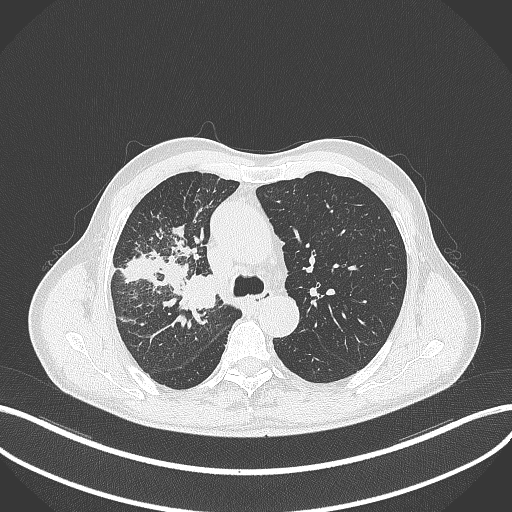
Chest CT, one axial slice. Slice 331 of 490 in the series (ordered by position). 120 kVp. Lung window (W 1500 / L -600 HU). 512 × 512 image matrix, field of view 400 × 400 mm. Patient: male, 69 years. Case-level facts recorded for this patient, not image findings: clinical TNM (as recorded): T2a N0 M0.
Outlined on this slice (rectangle marked by the reading radiologist):
- lung tumour (recorded histology: adenocarcinoma): bounding box [x1, y1, x2, y2] px = [182, 270, 223, 310]